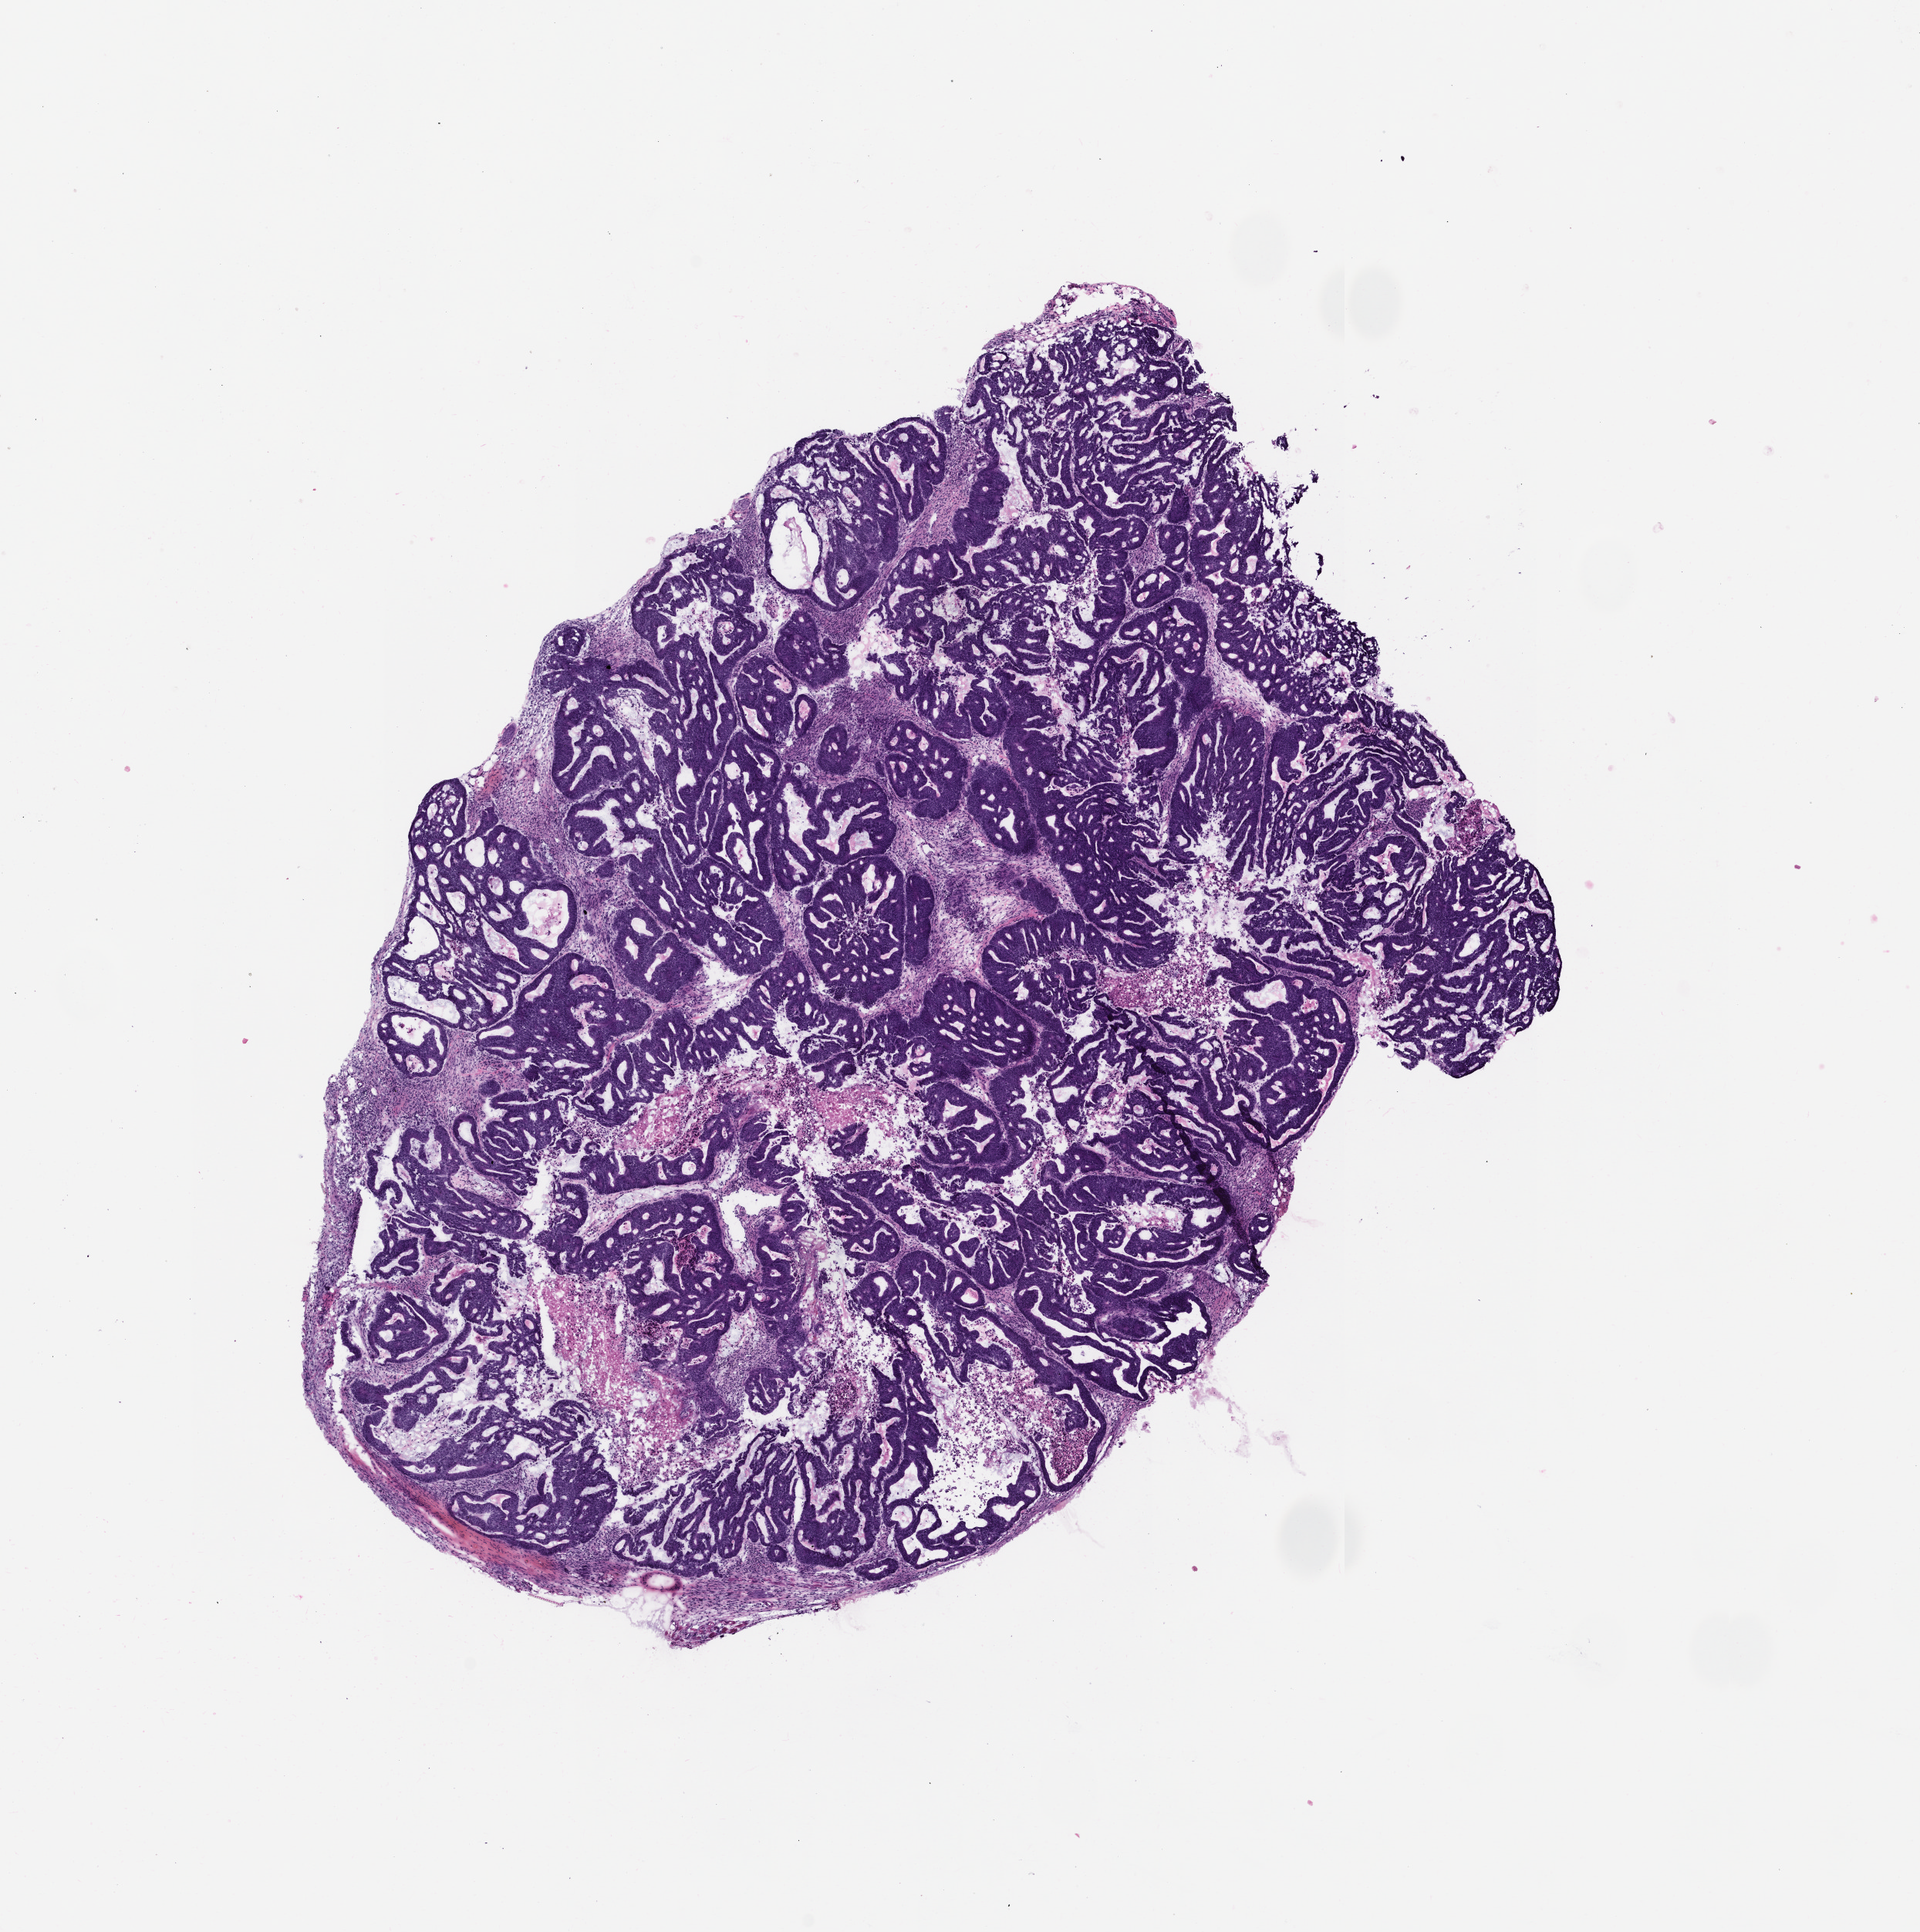
H&E whole-slide image of a patient-derived xenograft (PDX) tumor grown in a mouse, passage 6 — shown as a low-resolution overview of the whole scanned area (about 10.0 x 10.0 mm). FFPE section. Tumor site category: colon.
Originating patient diagnosis: Colon Adenocarcinoma.